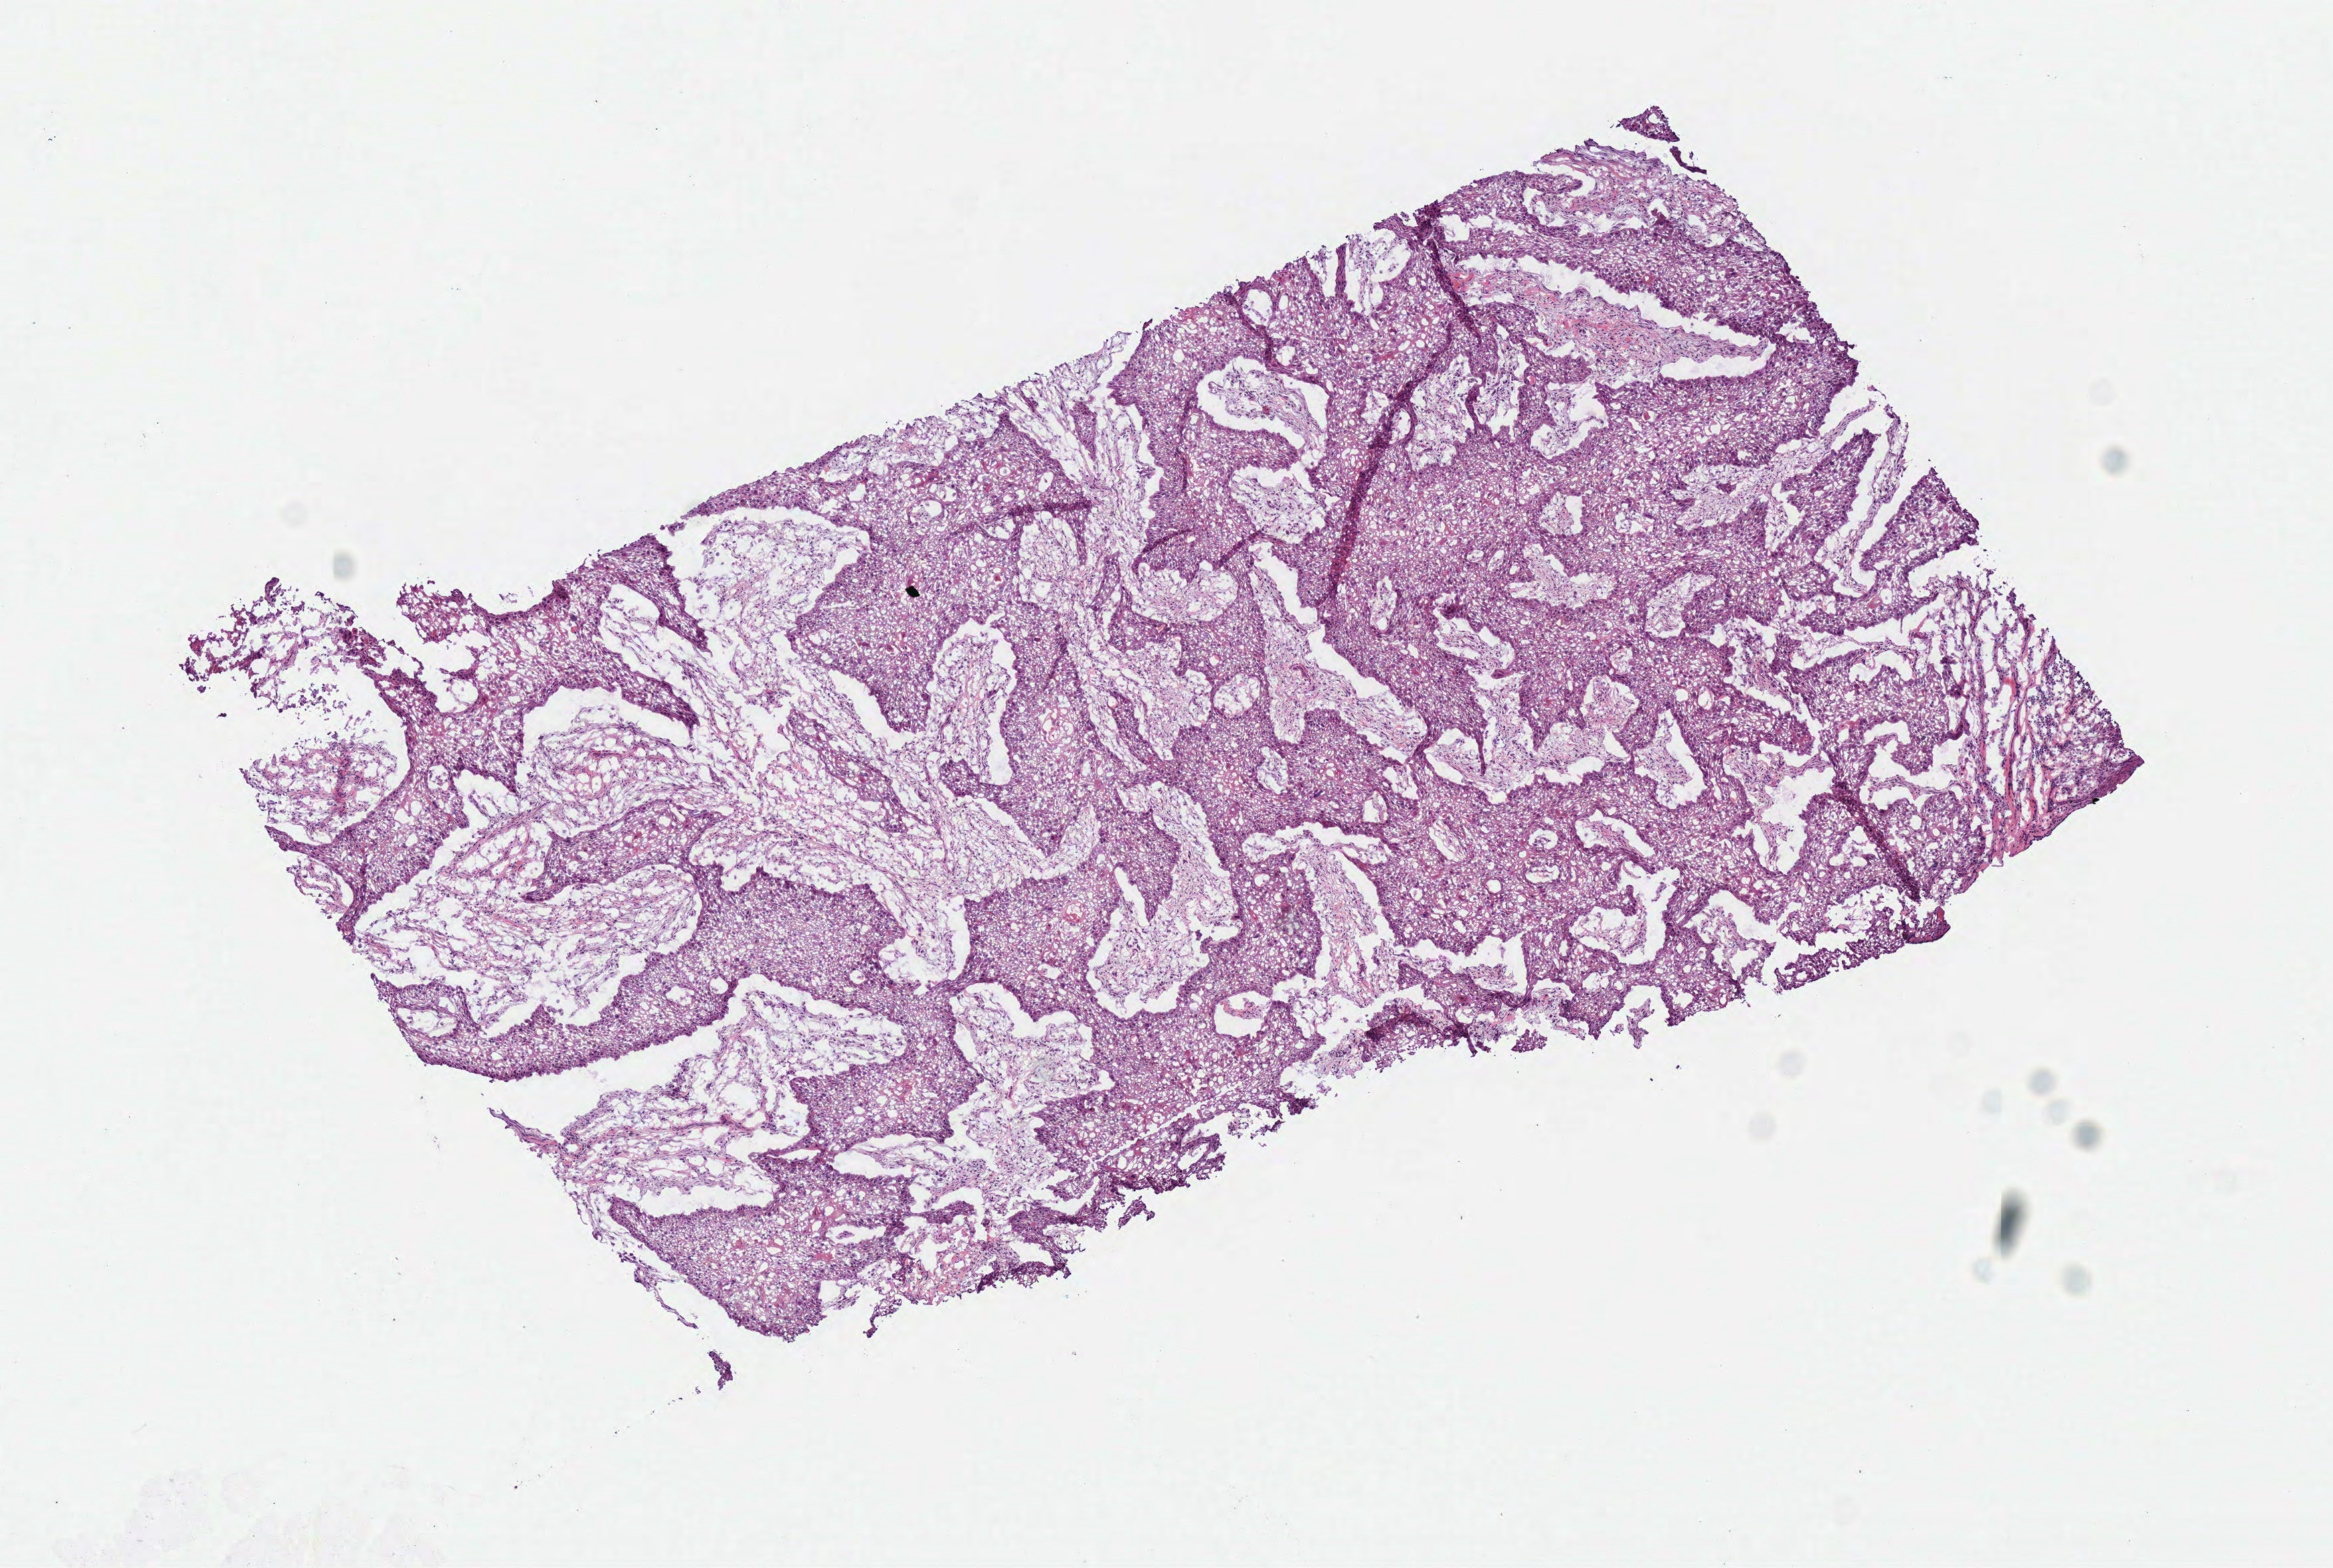
Digitized Hematoxylin and eosin (H&E) stained tissue section (whole slide) — whole scanned area (about 6.9 x 4.6 mm, from a 40x scan) shown as a low-resolution overview, frozen section from the bottom of the tissue portion, primary tumour sample from the head and neck. Male, age 54 years at initial diagnosis. Histologic grade: G3 (poorly differentiated). Composition of this section per pathologist review: tumour cells 85%, tumour nuclei 80%, normal cells 0%, stromal cells 15%, necrosis 0%.
AJCC pathologic stage: I (7th edition). Histologic diagnosis: Squamous cell carcinoma, NOS (overlapping lesion of lip, oral cavity and pharynx).